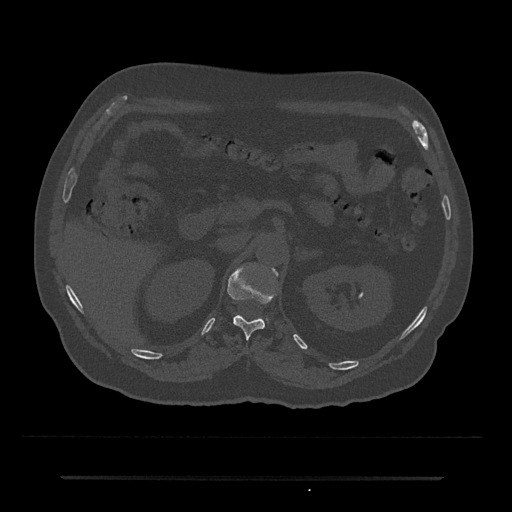
CT including the spine, one axial slice; slice 117 of 797 in the series (ordered by position); reconstruction kernel Br40s/3; bone window (W 1800 / L 400 HU); 512 × 512 image matrix. Patient: male, 69 years. Case-level facts recorded for this patient, not image findings: primary cancer: prostate.
Annotated regions visible in this slice (semi-automatic segmentation, software-assisted and operator-edited):
- T12 vertebra: bounding box (x1, y1, x2, y2) in pixels: (227, 265, 278, 339)